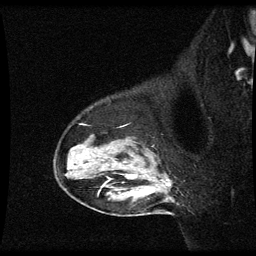
Breast MRI (dynamic contrast-enhanced), one sagittal slice; slice 46 of 60 in the series (ordered by position); dynamic contrast-enhanced series, image 2 of 3 at this slice position (ordered by acquisition); 1.5 T; TE 4.2 ms, TR 8.9 ms; 2 mm slice thickness; 256 × 256 image matrix, field of view 200 × 200 mm. Female patient, age 49 years. Case-level facts recorded for this patient, not image findings: setting: breast cancer imaged before/during neoadjuvant chemotherapy; receptor status: HR-positive, HER2-negative.
Annotated regions visible in this slice (semi-automatic segmentation, software-assisted and operator-edited):
- analysis volume of interest (the breast-tissue region the enhancement analysis was run in; not a lesion): bounding box <56,136,175,205> (left, top, right, bottom; pixels)
- tumour enhancement mask (voxels above the 70 % enhancement threshold inside the analysis volume of interest): <168,184,171,187>